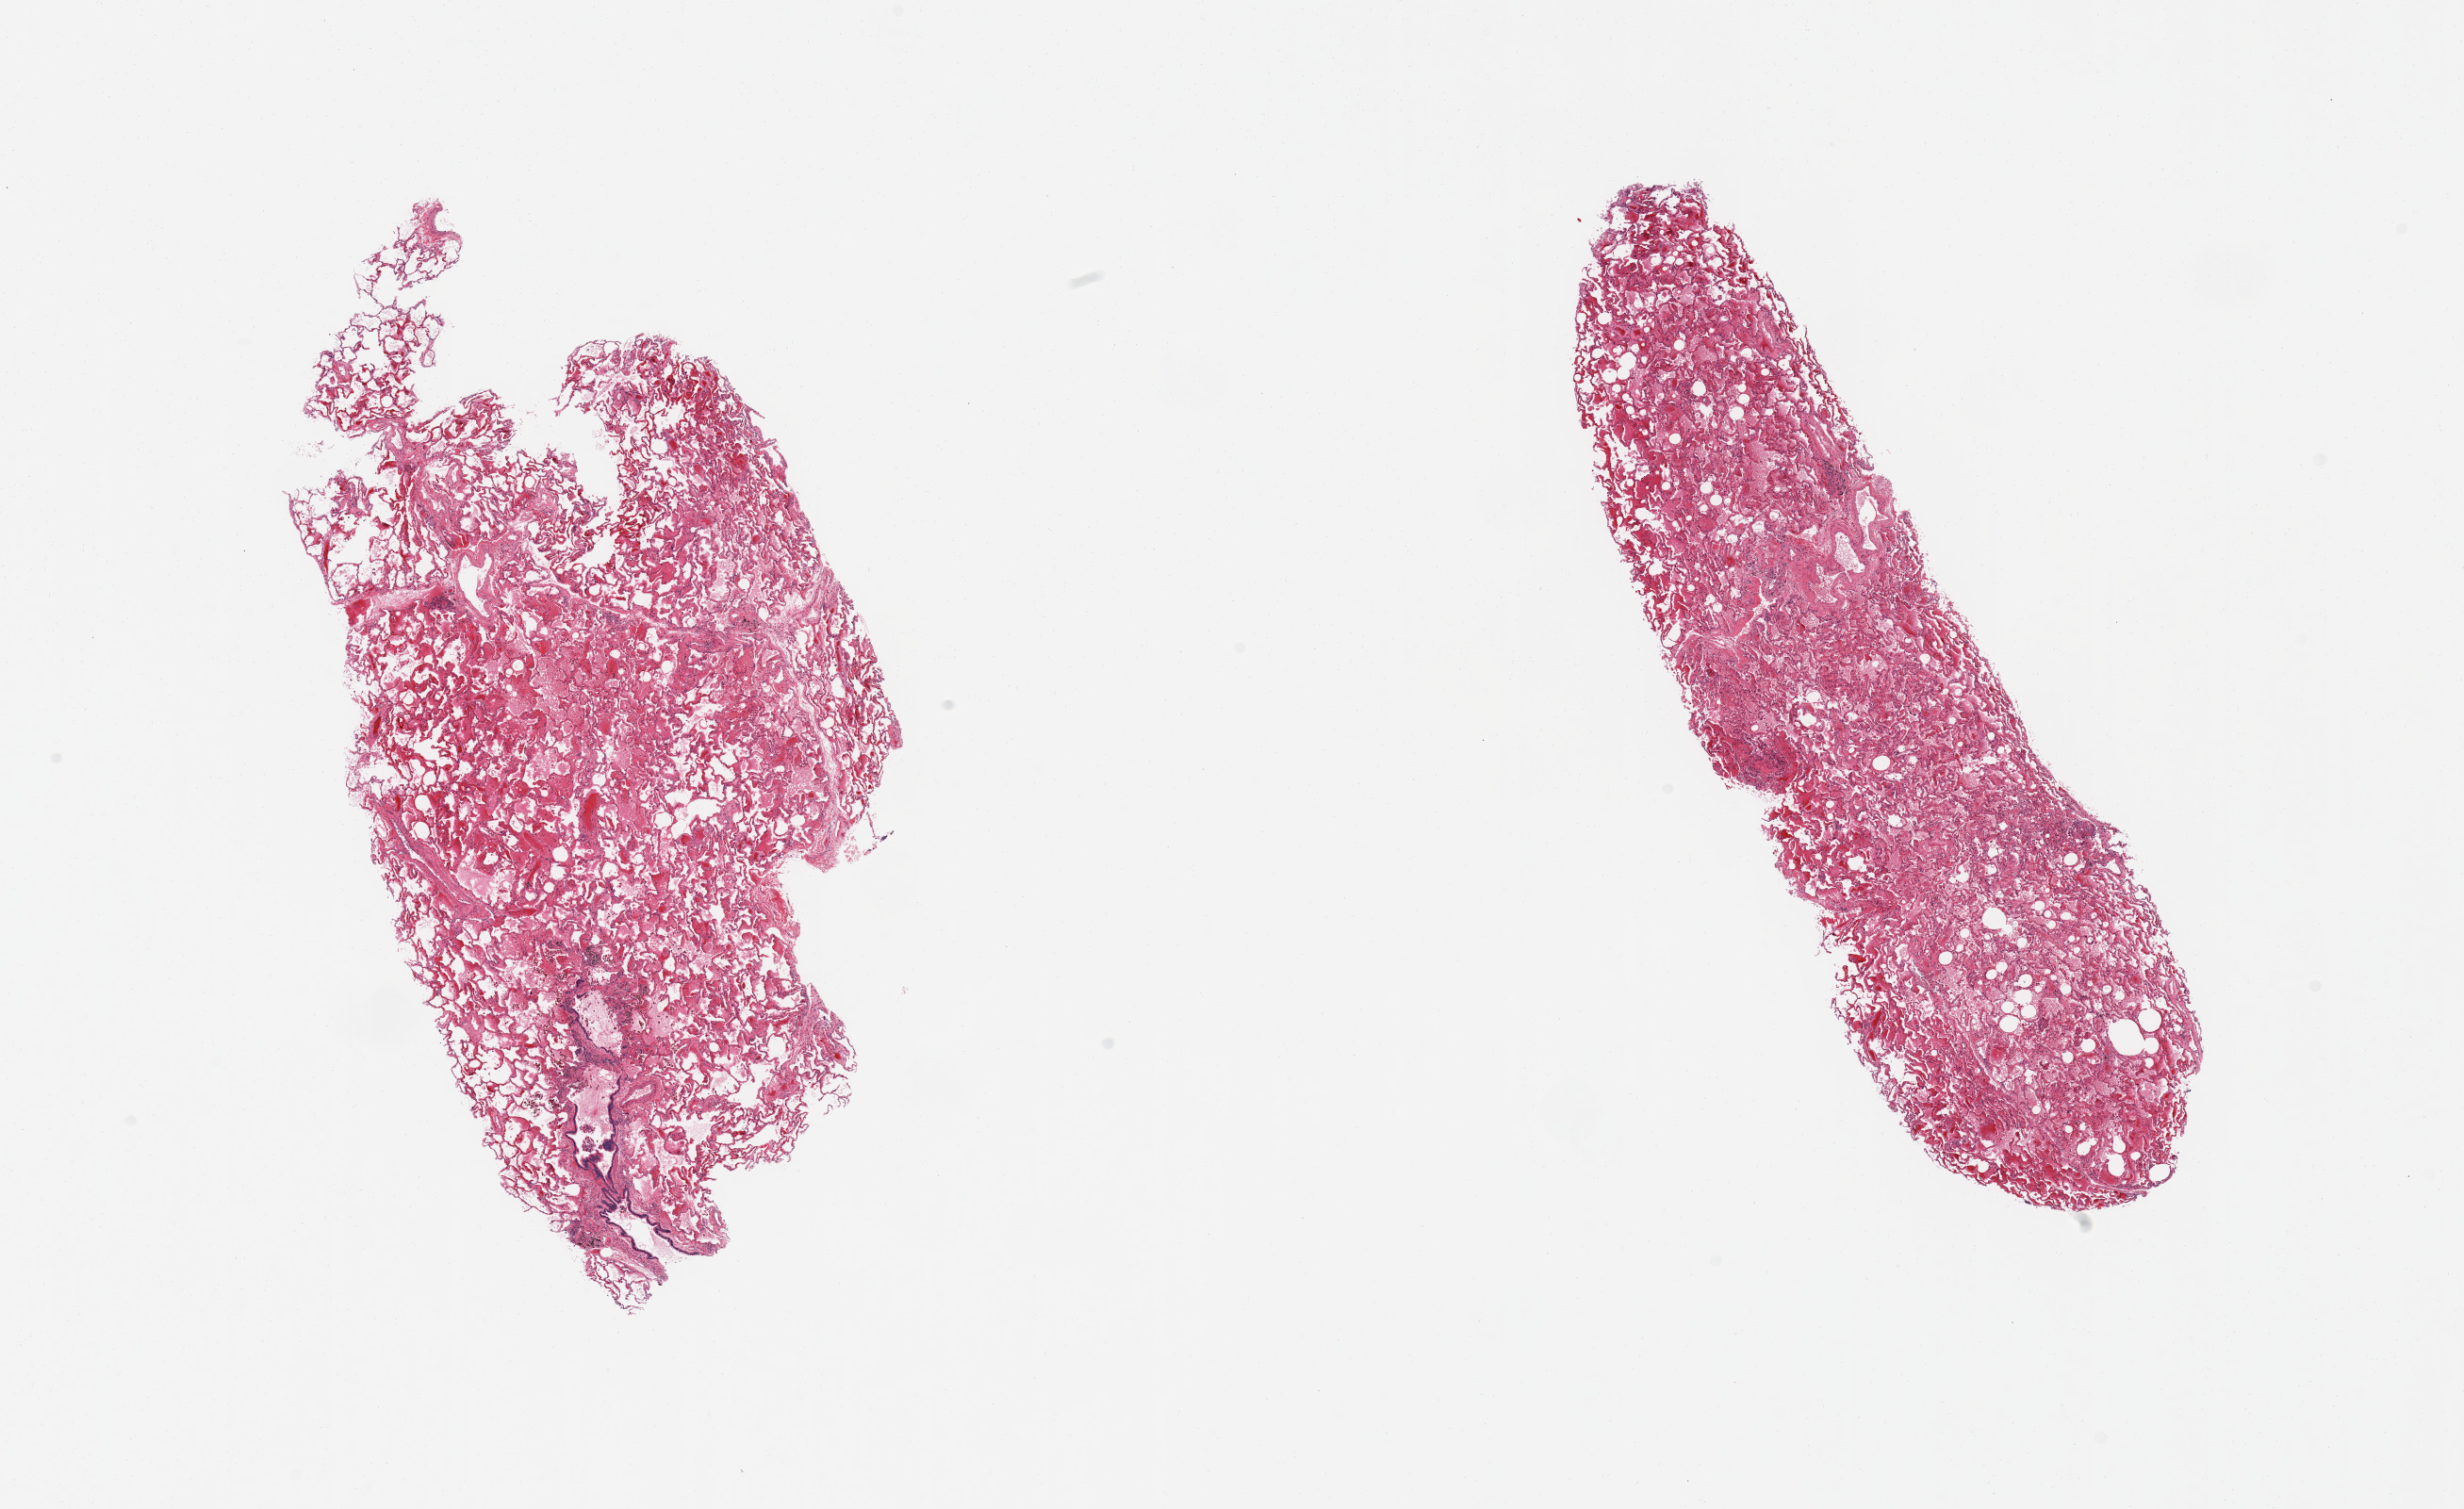
Digitized hematoxylin and eosin (H&E)-stained section — shown as a low-resolution overview of the whole scanned area (about 20.7 x 12.7 mm), PAXgene-fixed, paraffin-embedded tissue, sampled site (target tissue): lung, donor tissue sample. Donor: male.
Reviewer comment on this tissue sample: 2 pieces; moderate pulmonary edema; no chronic lesions.